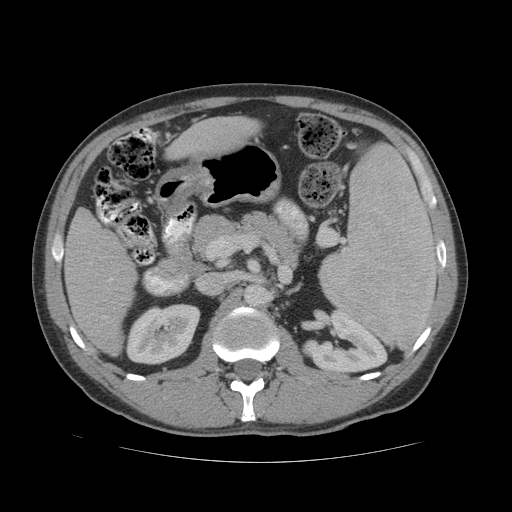
Contrast-enhanced abdominal CT (liver protocol), one axial slice; slice 23 of 81 in the series (ordered by position); 140 kVp; soft-tissue window (W 400 / L 40 HU); 2.5 mm slice thickness; 512 × 512 image matrix. Case-level facts recorded for this patient, not image findings: diagnosis: hepatocellular carcinoma (patient treated with transarterial chemoembolisation; whether this scan precedes or follows treatment is not stated here); TNM stage (as recorded): Stage-IVB; Child-Pugh class: B; tumour nodularity: multinodular.
Annotated regions visible in this slice (semi-automatically segmented with operator editing):
- liver parenchyma outside the tumour (the mass and vessels are separate outlines, so this box may not span the whole liver): bounding box <64,116,258,355> (left, top, right, bottom; pixels)
- liver vessels: <109,278,112,281>